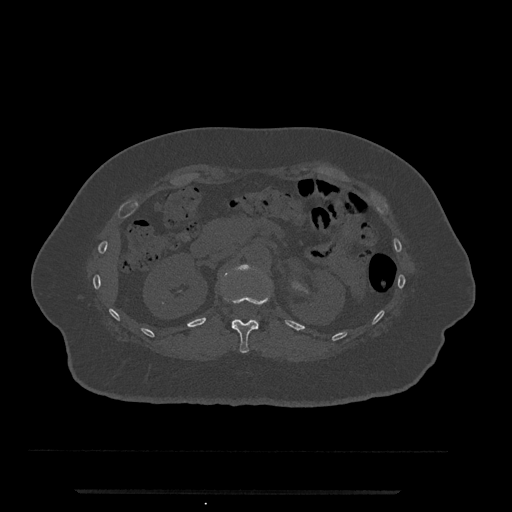
CT including the spine, one axial slice; position 147 of 797 along the scan axis; reconstruction kernel Br40s/3; 120 kVp; bone window (W 1800 / L 400 HU); 0.5 mm slice thickness; 512 × 512 image matrix. Female patient, age 51 years. From the clinical record (not read from this slice): primary cancer: neuro.
Outlined on this slice (semi-automatic segmentation, software-assisted and operator-edited):
- L1 vertebra: bounding box <235,265,252,271> (left, top, right, bottom; pixels)
- T12 vertebra: <223,294,270,353>